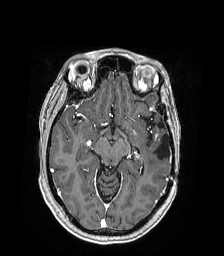
Brain MRI from a brain-tumour surgery series, one axial slice. T1-weighted post-contrast. 224 × 256 image matrix. From the clinical record (not read from this slice): histopathology: Astrocytoma; WHO grade: 4; IDH mutation: yes; tumour location: Left Temporal.
Annotated regions visible in this slice (outlined manually by an expert reader):
- tumour: box from (x=153, y=129) to (x=162, y=145) px